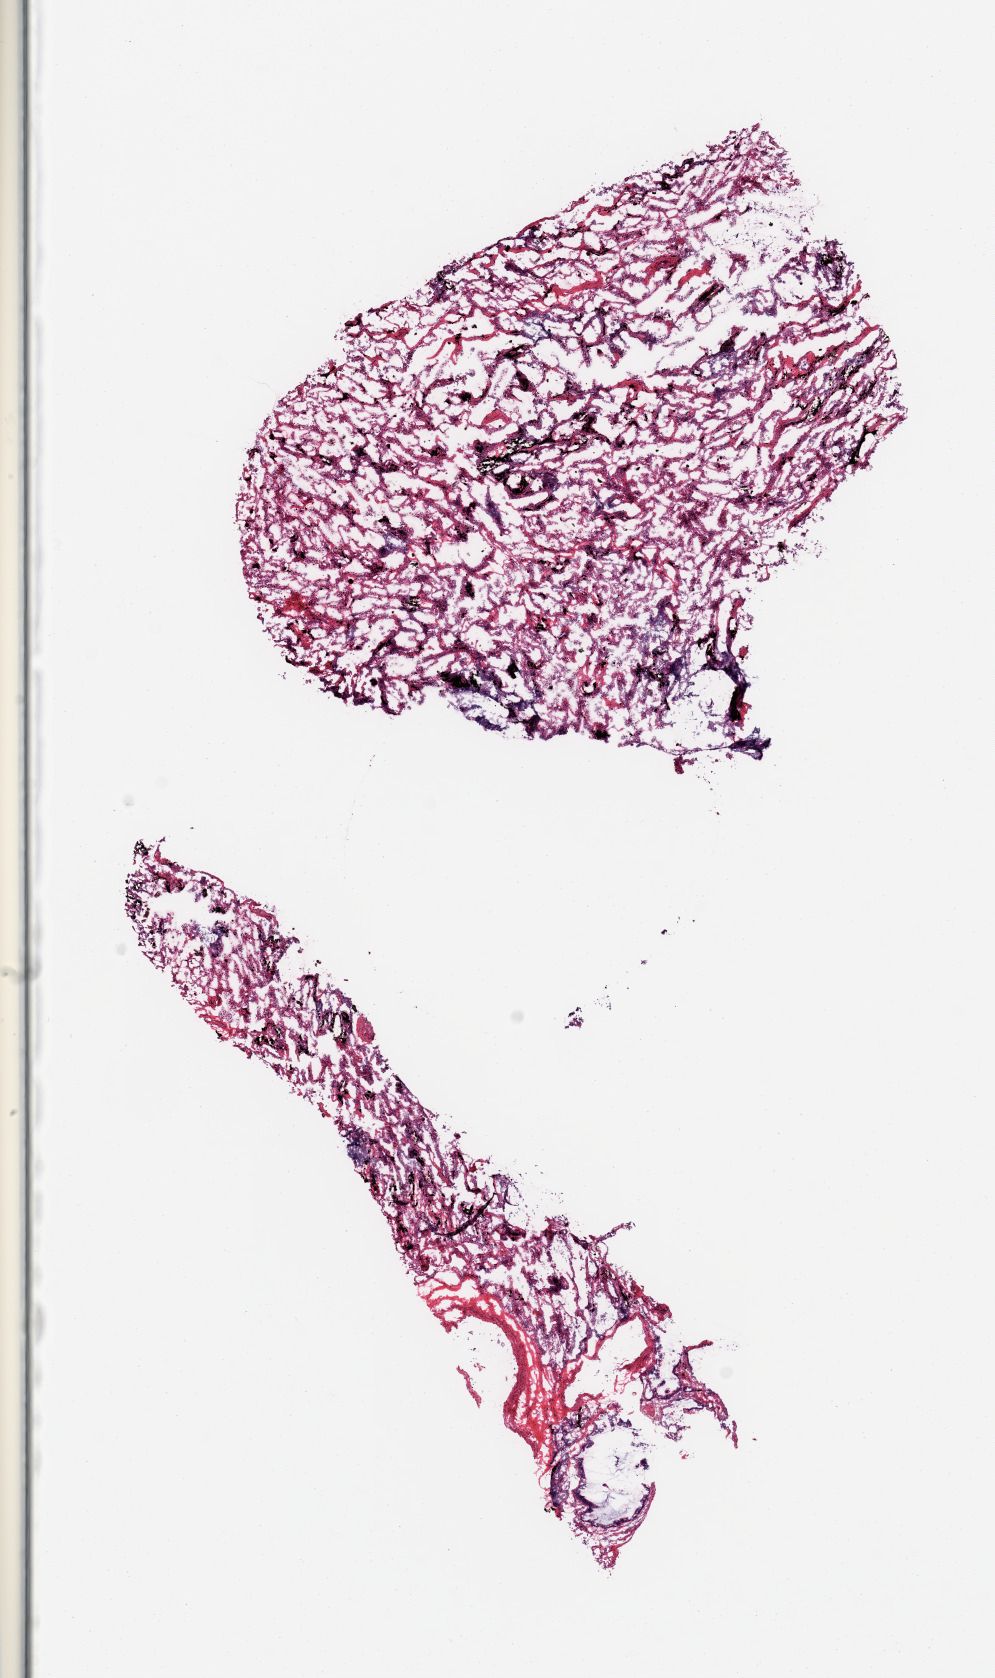
H&E whole-slide image, brightfield, whole scanned area (about 7.9 x 13.3 mm, acquisition: 20x scan) shown as a low-resolution overview, frozen section, target tissue: lung, donor tissue sample. Donor sex: female.
Review note (as recorded): 2 pieces; lung parenchyma without the fibrosis and other changes seen in the PAXgene samples.